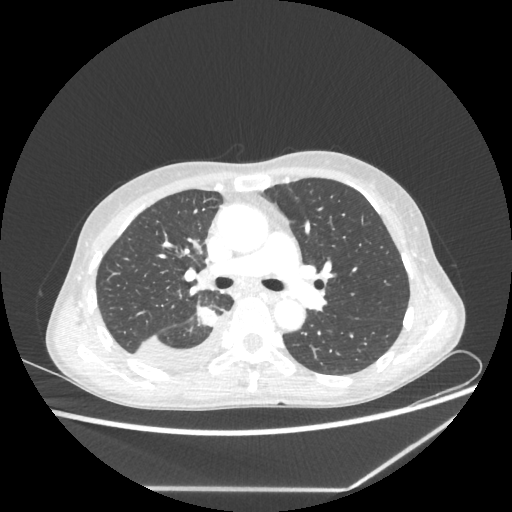
Chest CT, one axial slice. Slice 142 of 237 in the series (ordered by position). 80 kVp. Lung window (W 1500 / L -600 HU). 1.25 mm slice thickness. 512 × 512 image matrix, field of view 364 × 364 mm. Patient: female, 59 years. Case-level facts recorded for this patient, not image findings: clinical TNM (as recorded): T1c N1 M1.
Structures marked on this image (bounding box drawn by a radiologist):
- lung tumour (recorded histology: adenocarcinoma): bounding box (x1, y1, x2, y2) in pixels: (194, 303, 217, 329)